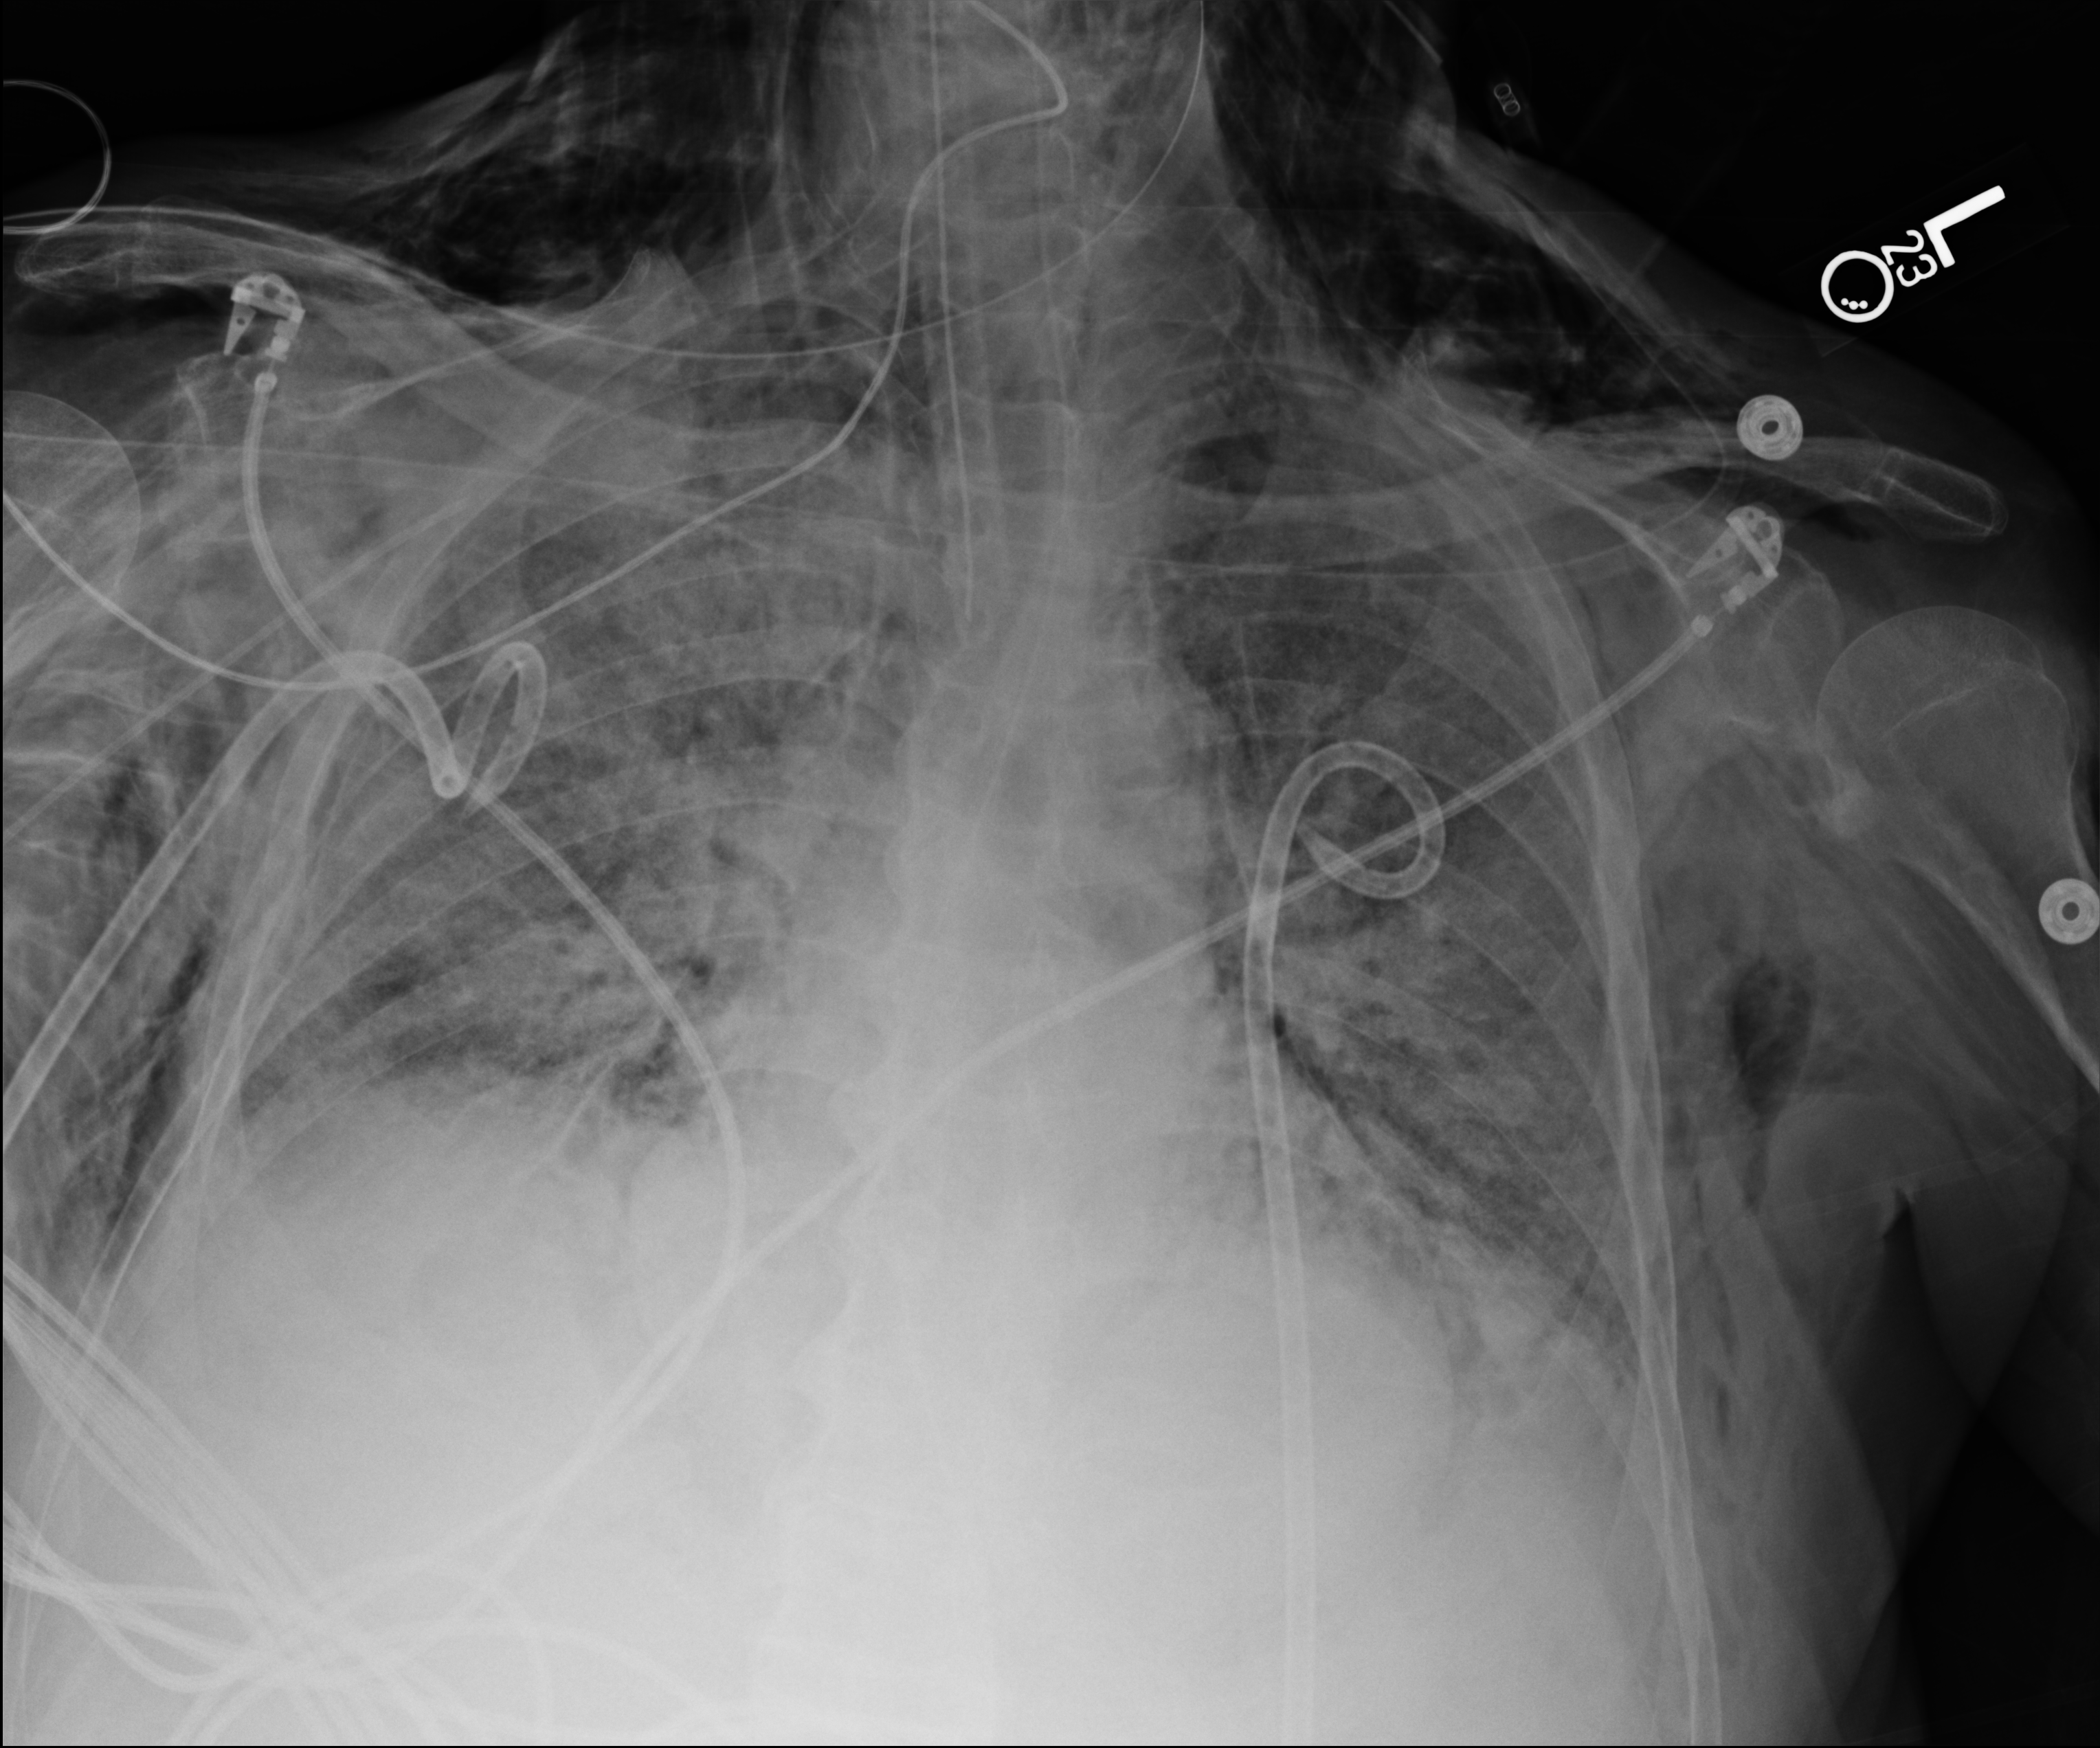
Bedside chest radiograph (computed radiography), anteroposterior (AP) projection. Male patient hospitalised with COVID-19, age 75–90 years.
Admission-level facts for this patient (not findings on this image; timing relative to this image not recorded): mechanically ventilated during this hospital stay: yes; admitted to intensive care during this hospital stay: yes.